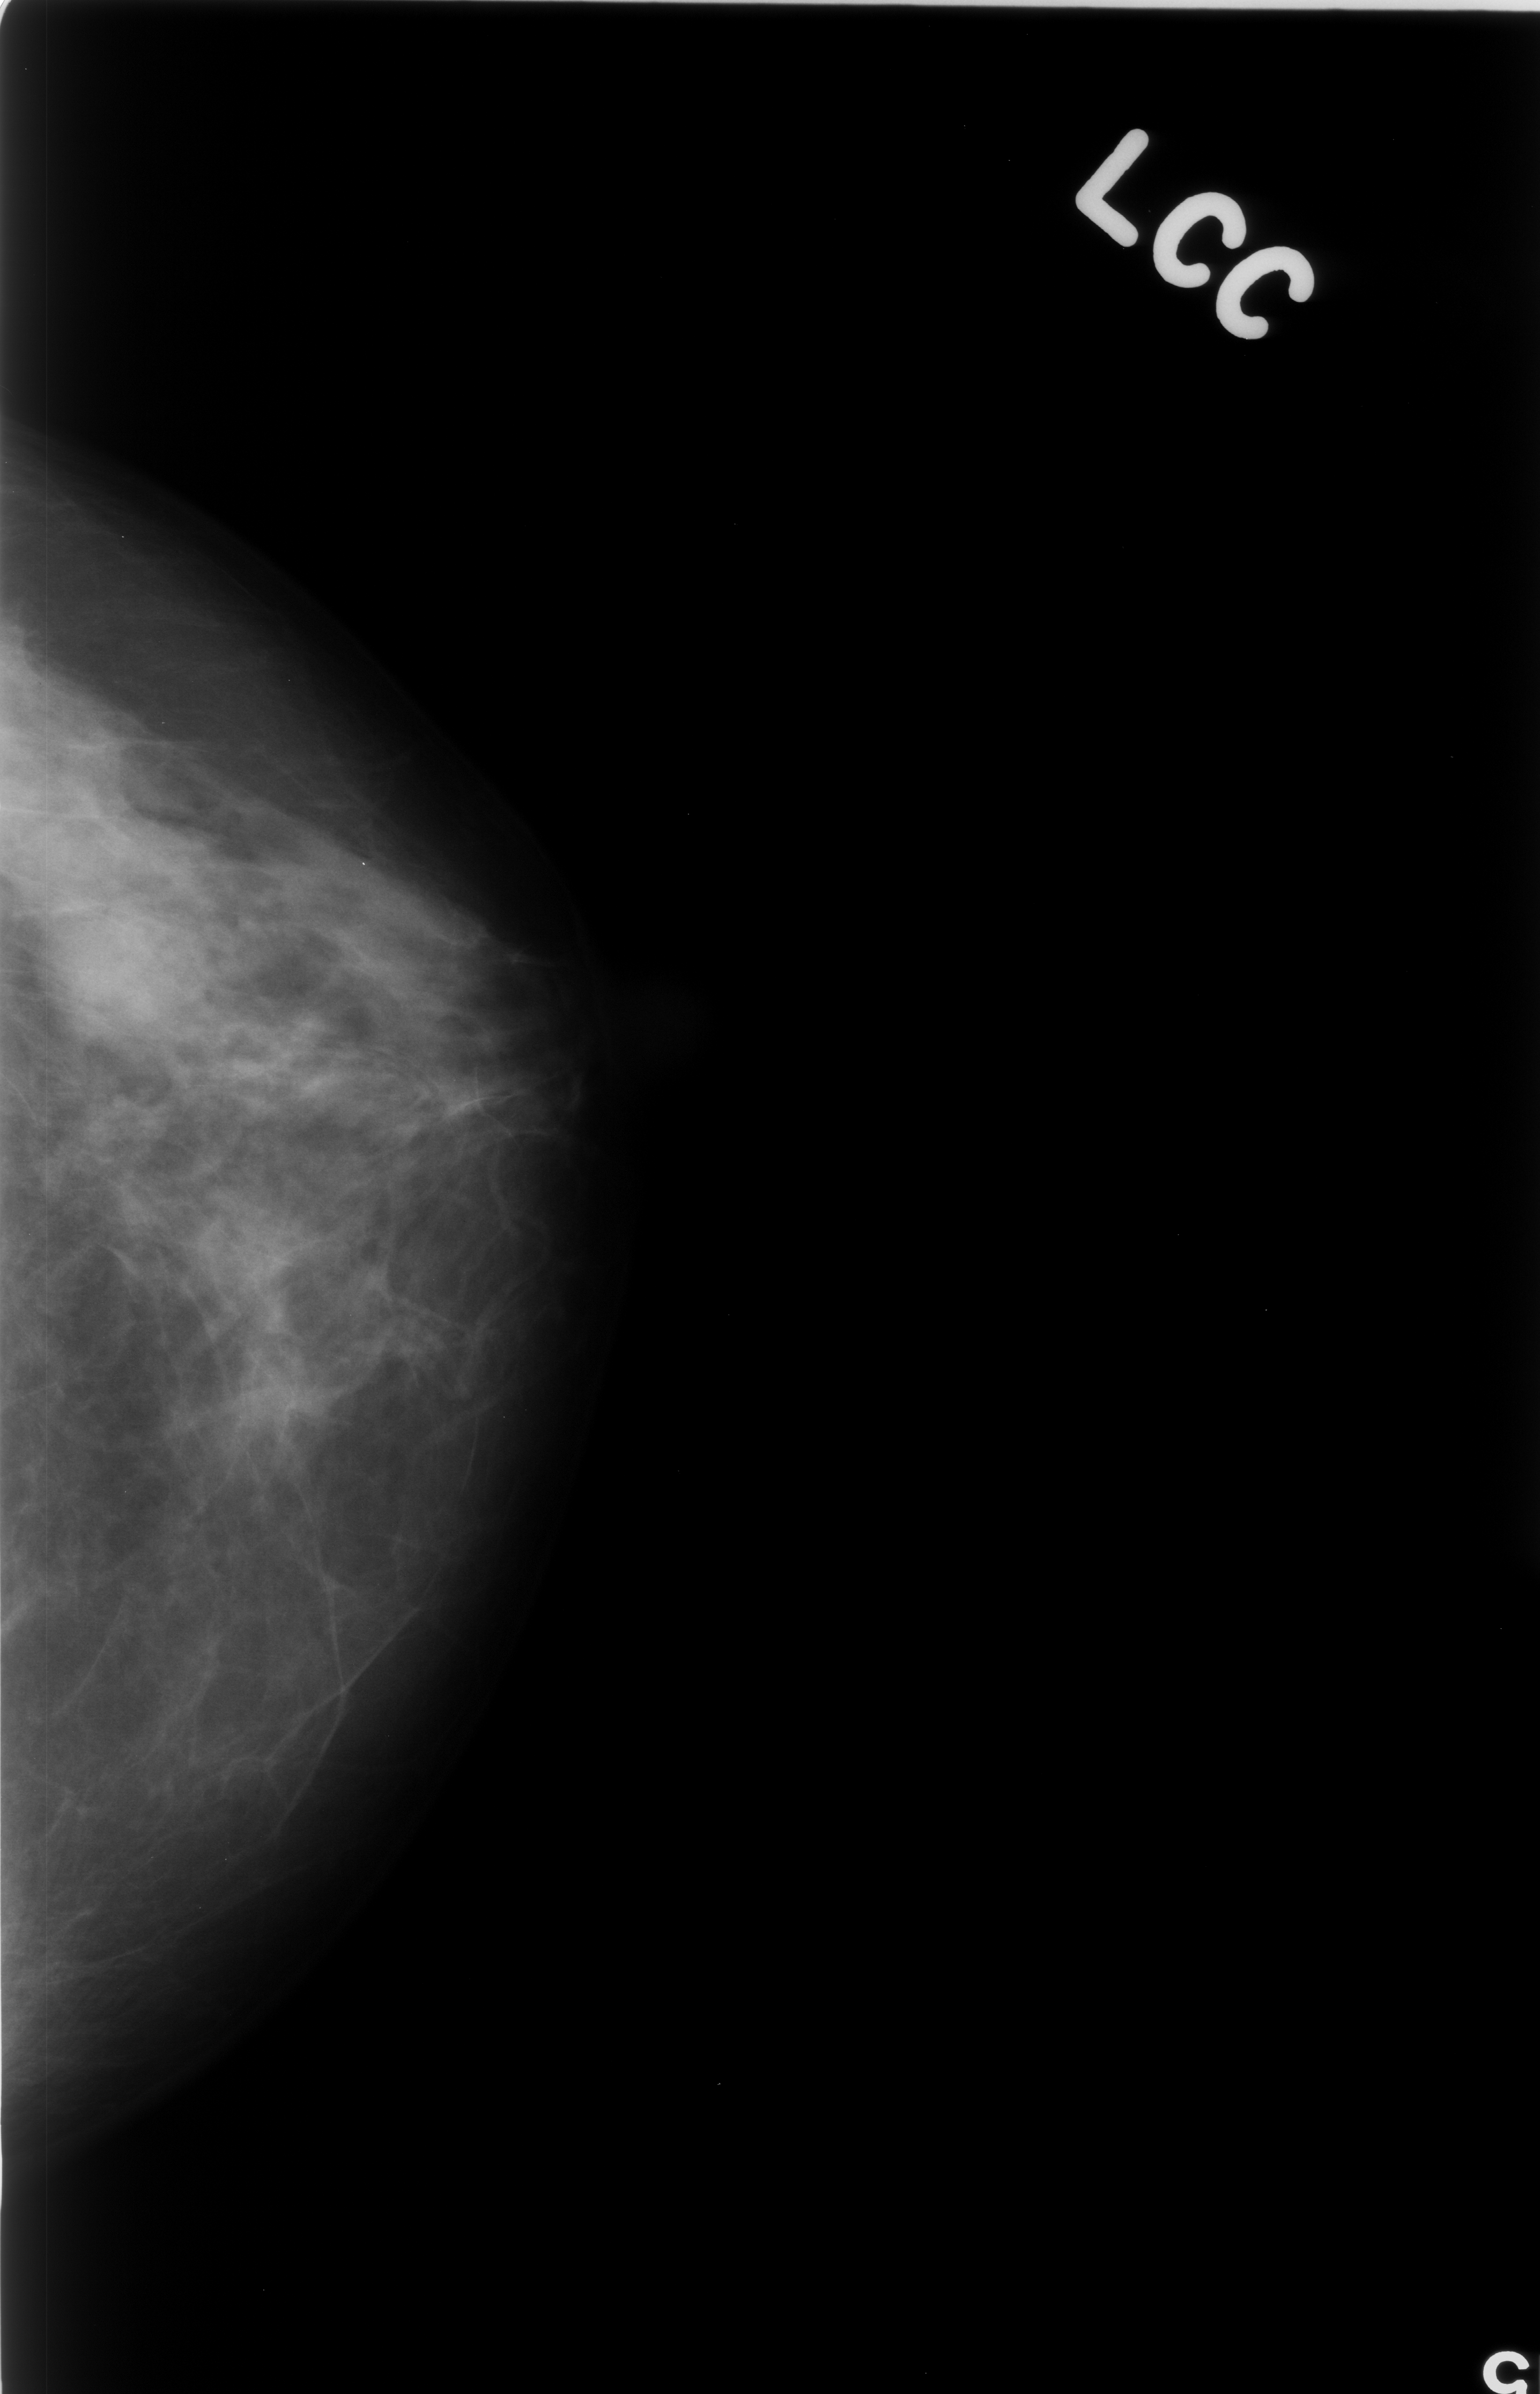
Scanned film-screen mammogram. Left breast. CC view. BI-RADS breast density category 2 (scale 1–4). 1540 × 2394 image matrix.
Marked abnormalities (boxes around the expert regions of interest):
- mass, shape oval, margins obscured; BI-RADS assessment category 4; subtlety rating 4 on a 1 (subtle) to 5 (obvious) scale; pathology (as recorded): benign: bounding box [x1, y1, x2, y2] px = [38, 861, 213, 1034]